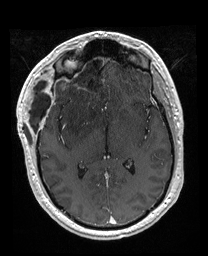
Brain MRI from a brain-tumour surgery series, one axial slice; slice 97 of 176 in the series (ordered by position); T1-weighted post-contrast; 208 × 256 image matrix. From the clinical record (not read from this slice): histopathology: Astrocytoma; WHO grade: 4; IDH mutation: yes; tumour location: Right Orbitofrontal Anterior Temporal Insular.
Annotated regions visible in this slice (expert manual segmentation):
- previous resection cavity: bounding box <56,52,106,86> (left, top, right, bottom; pixels)